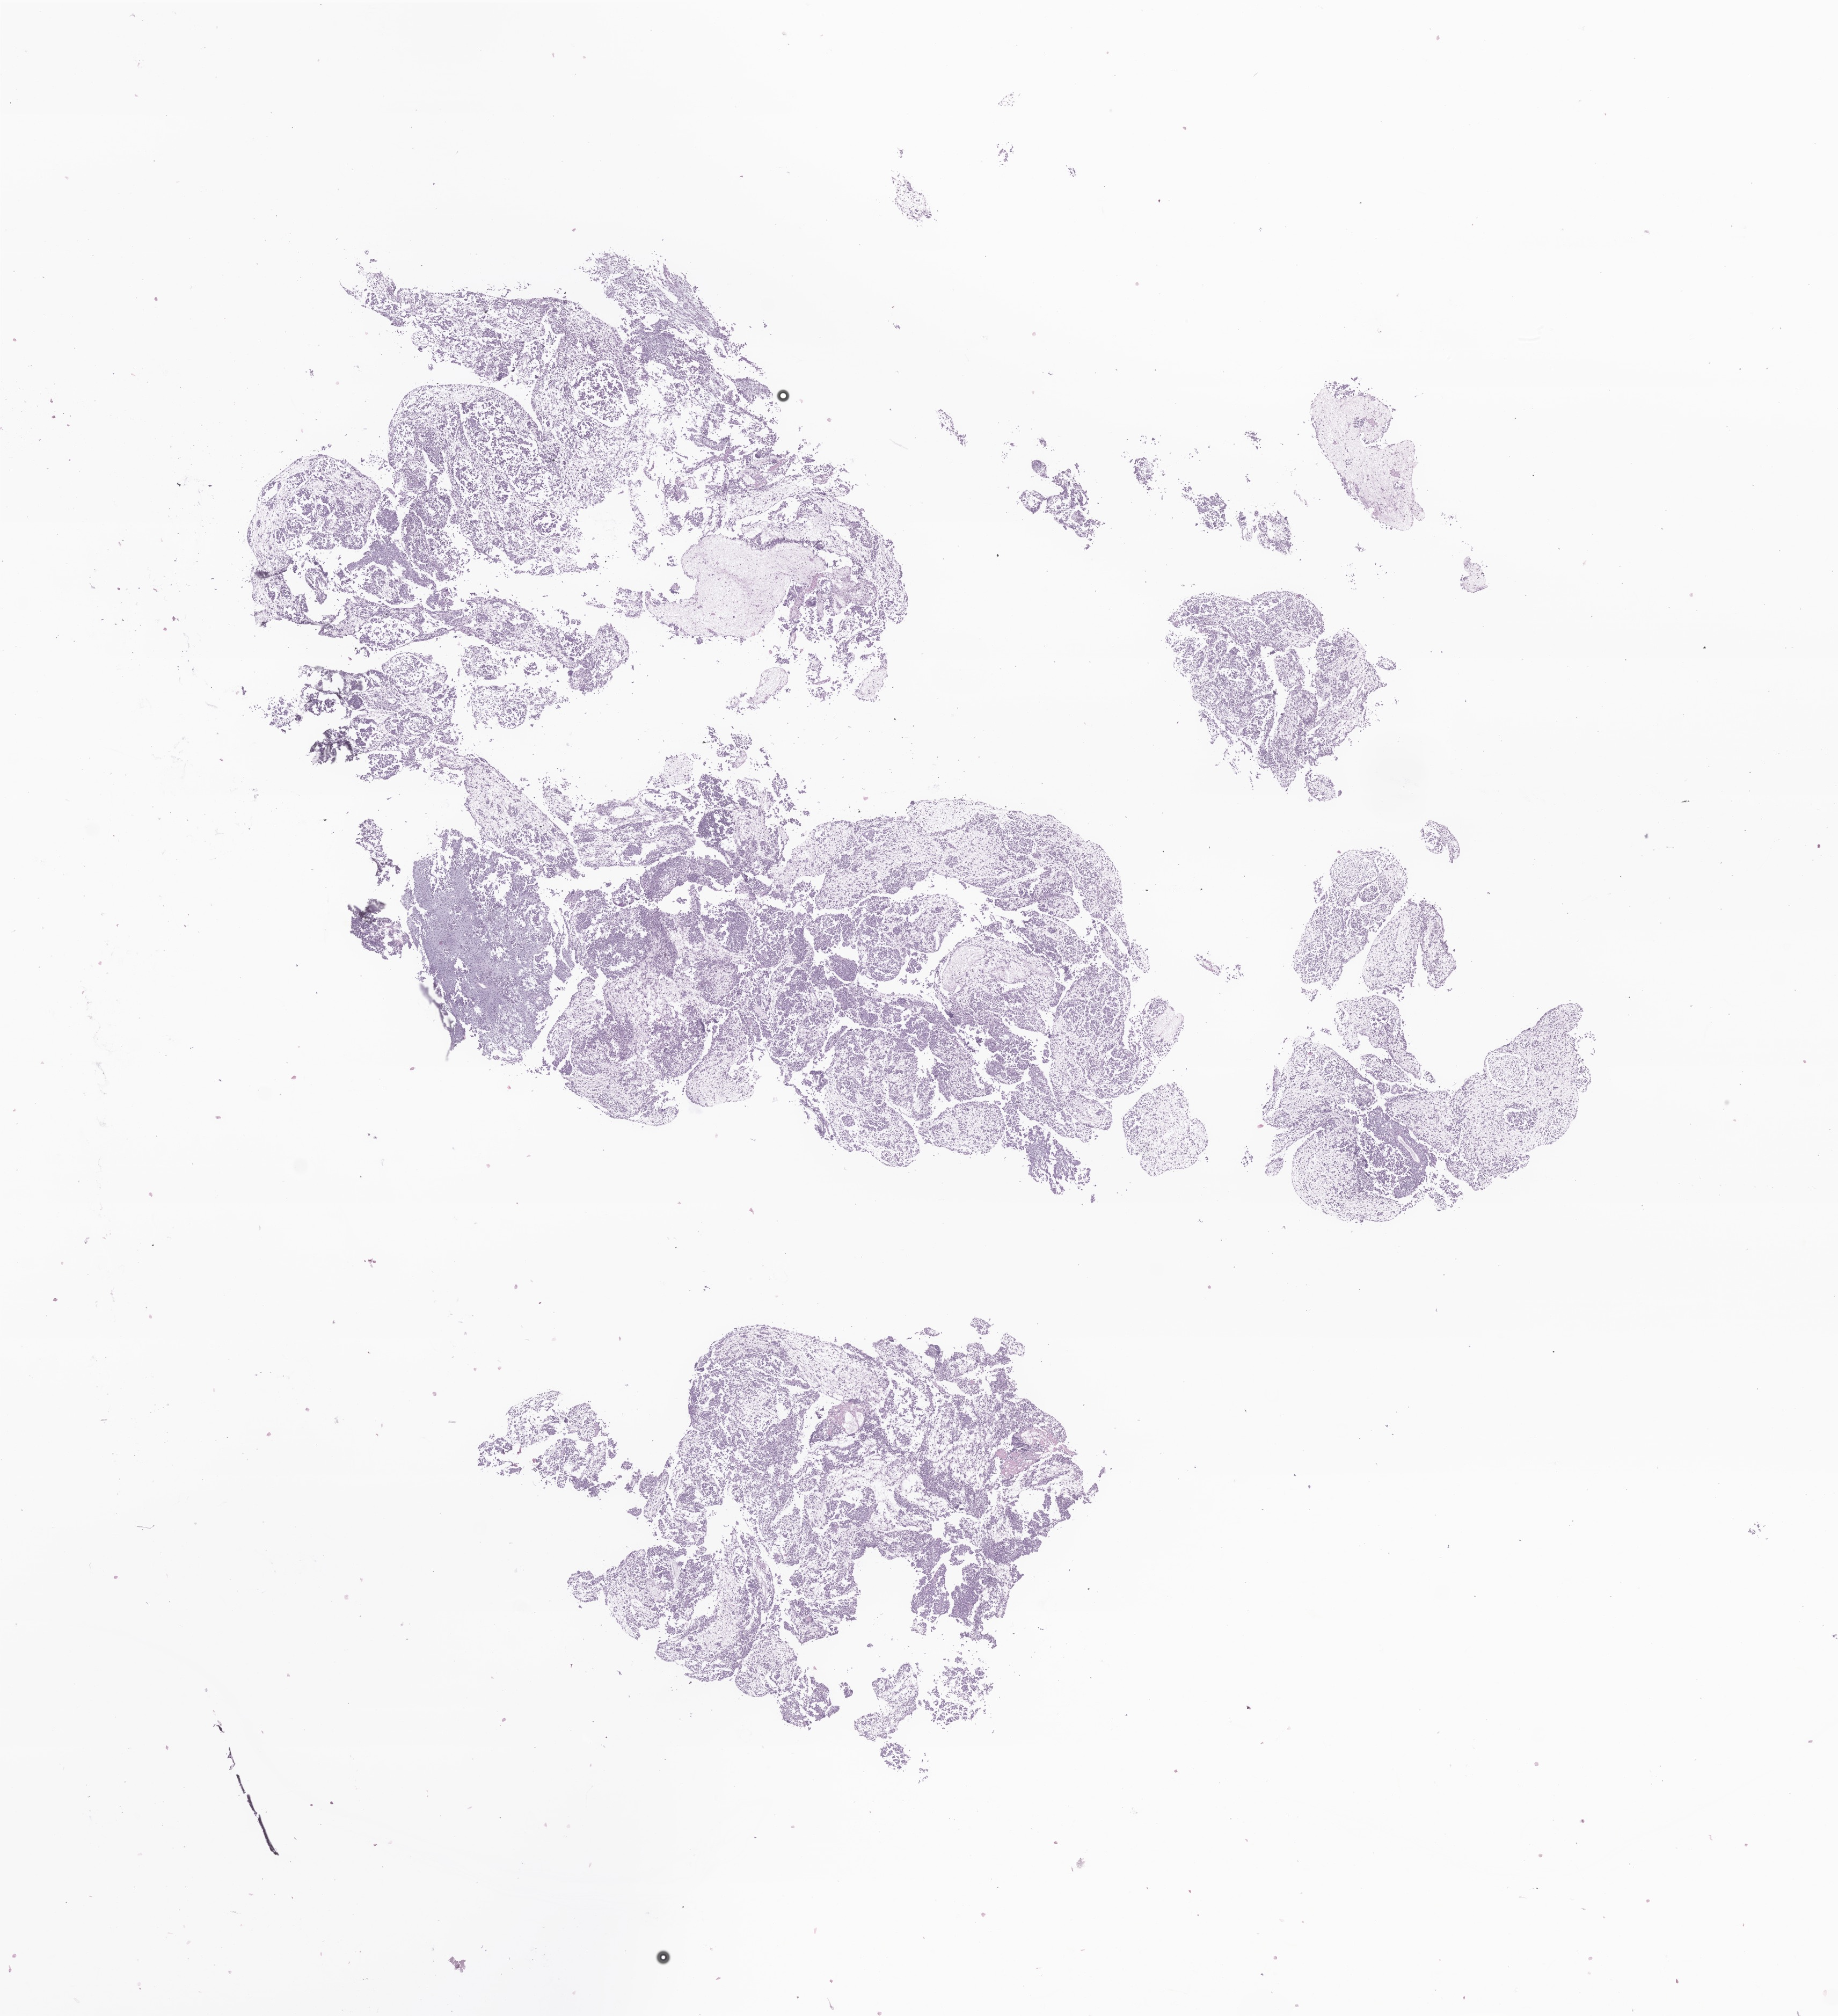
Digitized haematoxylin and eosin-stained section of tumor tissue from the brain, shown as a low-resolution overview of the whole scanned area (about 14.4 x 15.8 mm). Formalin-fixed paraffin-embedded section. Male patient, age 401 days (about 1.1 years).
Diagnosis: Atypical teratoid/rhabdoid tumor.